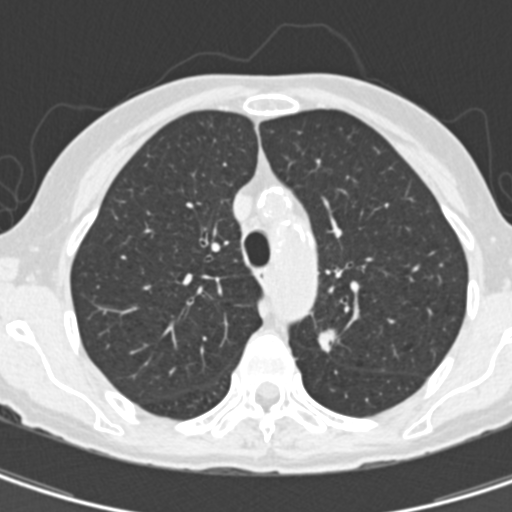
Low-dose screening chest CT, one axial slice; position 112 of 157 along the scan axis; reconstruction kernel B30f; 120 kVp; lung window (W 1500 / L -600 HU); 2 mm slice thickness; 512 × 512 image matrix.
Outlined on this slice (expert manual segmentation):
- lesion 1 (tumor, upper lobe of left lung): bounding box [x1, y1, x2, y2] px = [318, 329, 339, 353]